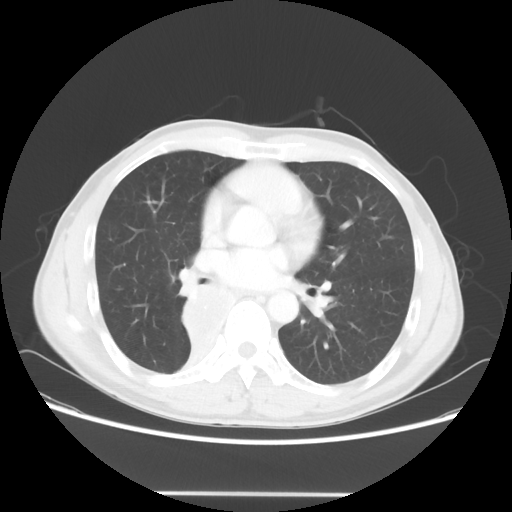
Chest CT, one axial slice. Position 31 of 62 along the scan axis. 120 kVp. Lung window (W 1500 / L -600 HU). 5 mm slice thickness. 512 × 512 image matrix, field of view 393 × 393 mm. Male patient, age 47 years. Case-level facts recorded for this patient, not image findings: clinical TNM (as recorded): T2 N0 M0.
Structures marked on this image (rectangle marked by the reading radiologist):
- lung tumour (recorded histology: squamous cell carcinoma): bounding box (x1, y1, x2, y2) in pixels: (172, 278, 234, 348)